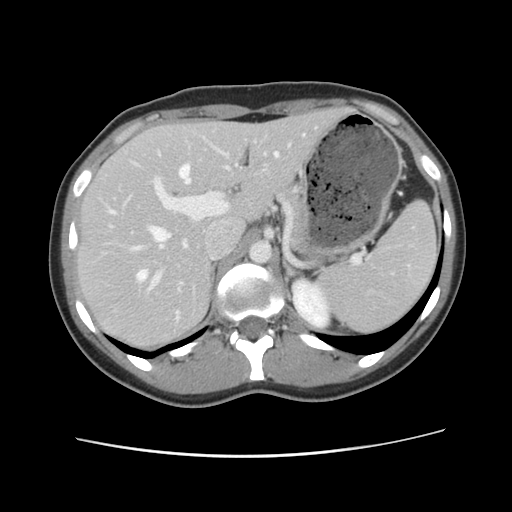
Contrast-enhanced abdominal CT, one axial slice. Position 73 of 134 along the scan axis. 120 kVp. Intravenous contrast given. Soft-tissue window (W 400 / L 40 HU). 2.5 mm slice thickness. 512 × 512 image matrix, field of view 339 × 339 mm. Female patient, age 33 years. Case-level facts recorded for this patient, not image findings: diagnosis: colorectal cancer liver metastases, imaged before liver resection; multiple liver metastases: yes; largest metastasis: 4.5 cm; disease in both lobes: yes.
Annotated regions visible in this slice (outlined manually by an expert reader):
- hepatic veins: box from (x=111, y=153) to (x=279, y=320) px
- liver: (x=78, y=109)–(x=347, y=351)
- planned liver remnant (the part of the liver to remain after resection): (x=78, y=109)–(x=346, y=351)
- portal vein (with intrahepatic branches): (x=151, y=139)–(x=293, y=281)